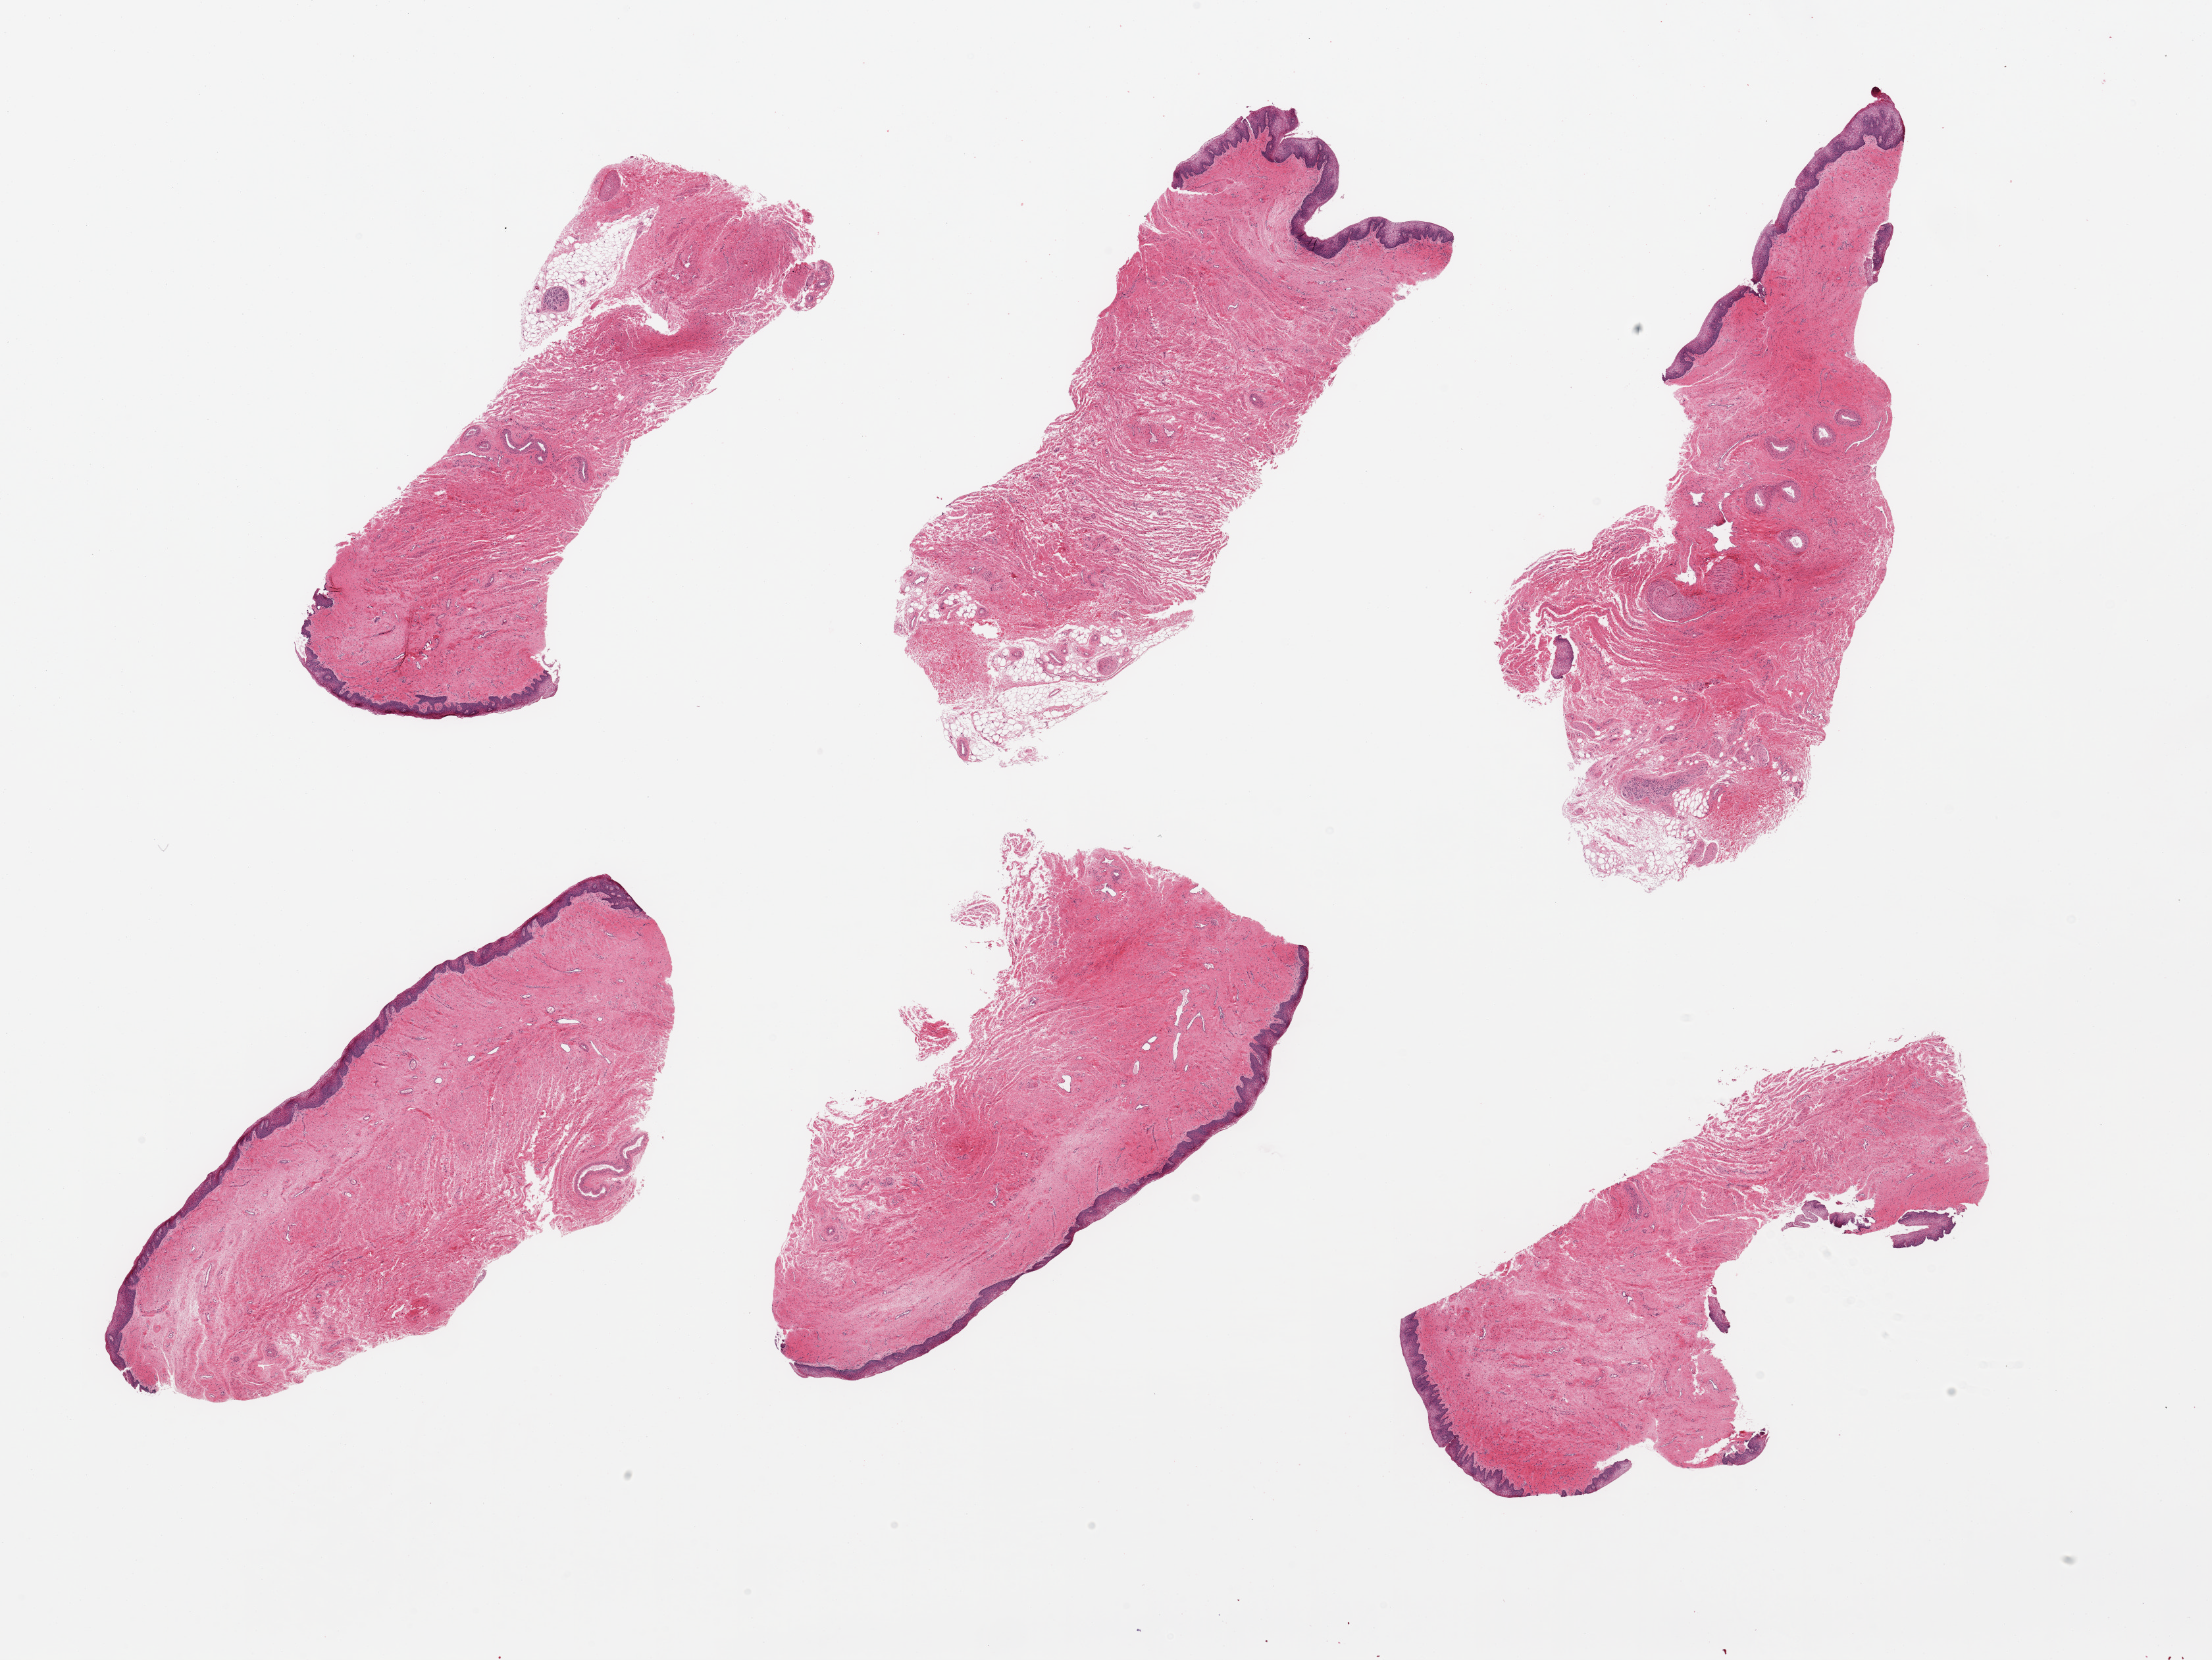
Digitized hematoxylin and eosin (H&E)-stained section — a low-resolution overview of the entire scanned area, about 26.6 x 19.9 mm. PAXgene-fixed, paraffin-embedded tissue. Target tissue: vagina. Donor tissue sample. Donor: female.
Review note (as recorded): 6 pieces, squamous mucosa up to ~0.25mm.